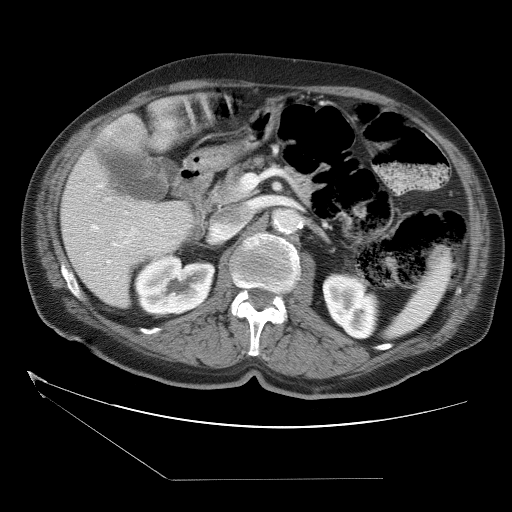
Contrast-enhanced abdominal CT (liver protocol), one axial slice; 120 kVp; one of 2 acquisitions stored at this slice position; soft-tissue window (W 400 / L 40 HU); 5 mm slice thickness; 512 × 512 image matrix, field of view 400 × 400 mm. Case-level facts recorded for this patient, not image findings: diagnosis: hepatocellular carcinoma (patient treated with transarterial chemoembolisation; whether this scan precedes or follows treatment is not stated here); TNM stage (as recorded): Stage-II; Child-Pugh class: A.
Outlined on this slice (semi-automatic segmentation, software-assisted and operator-edited):
- liver parenchyma outside the tumour (the mass and vessels are separate outlines, so this box may not span the whole liver): bounding box (x1, y1, x2, y2) in pixels: (60, 114, 192, 306)
- liver vessels: (91, 224, 141, 303)